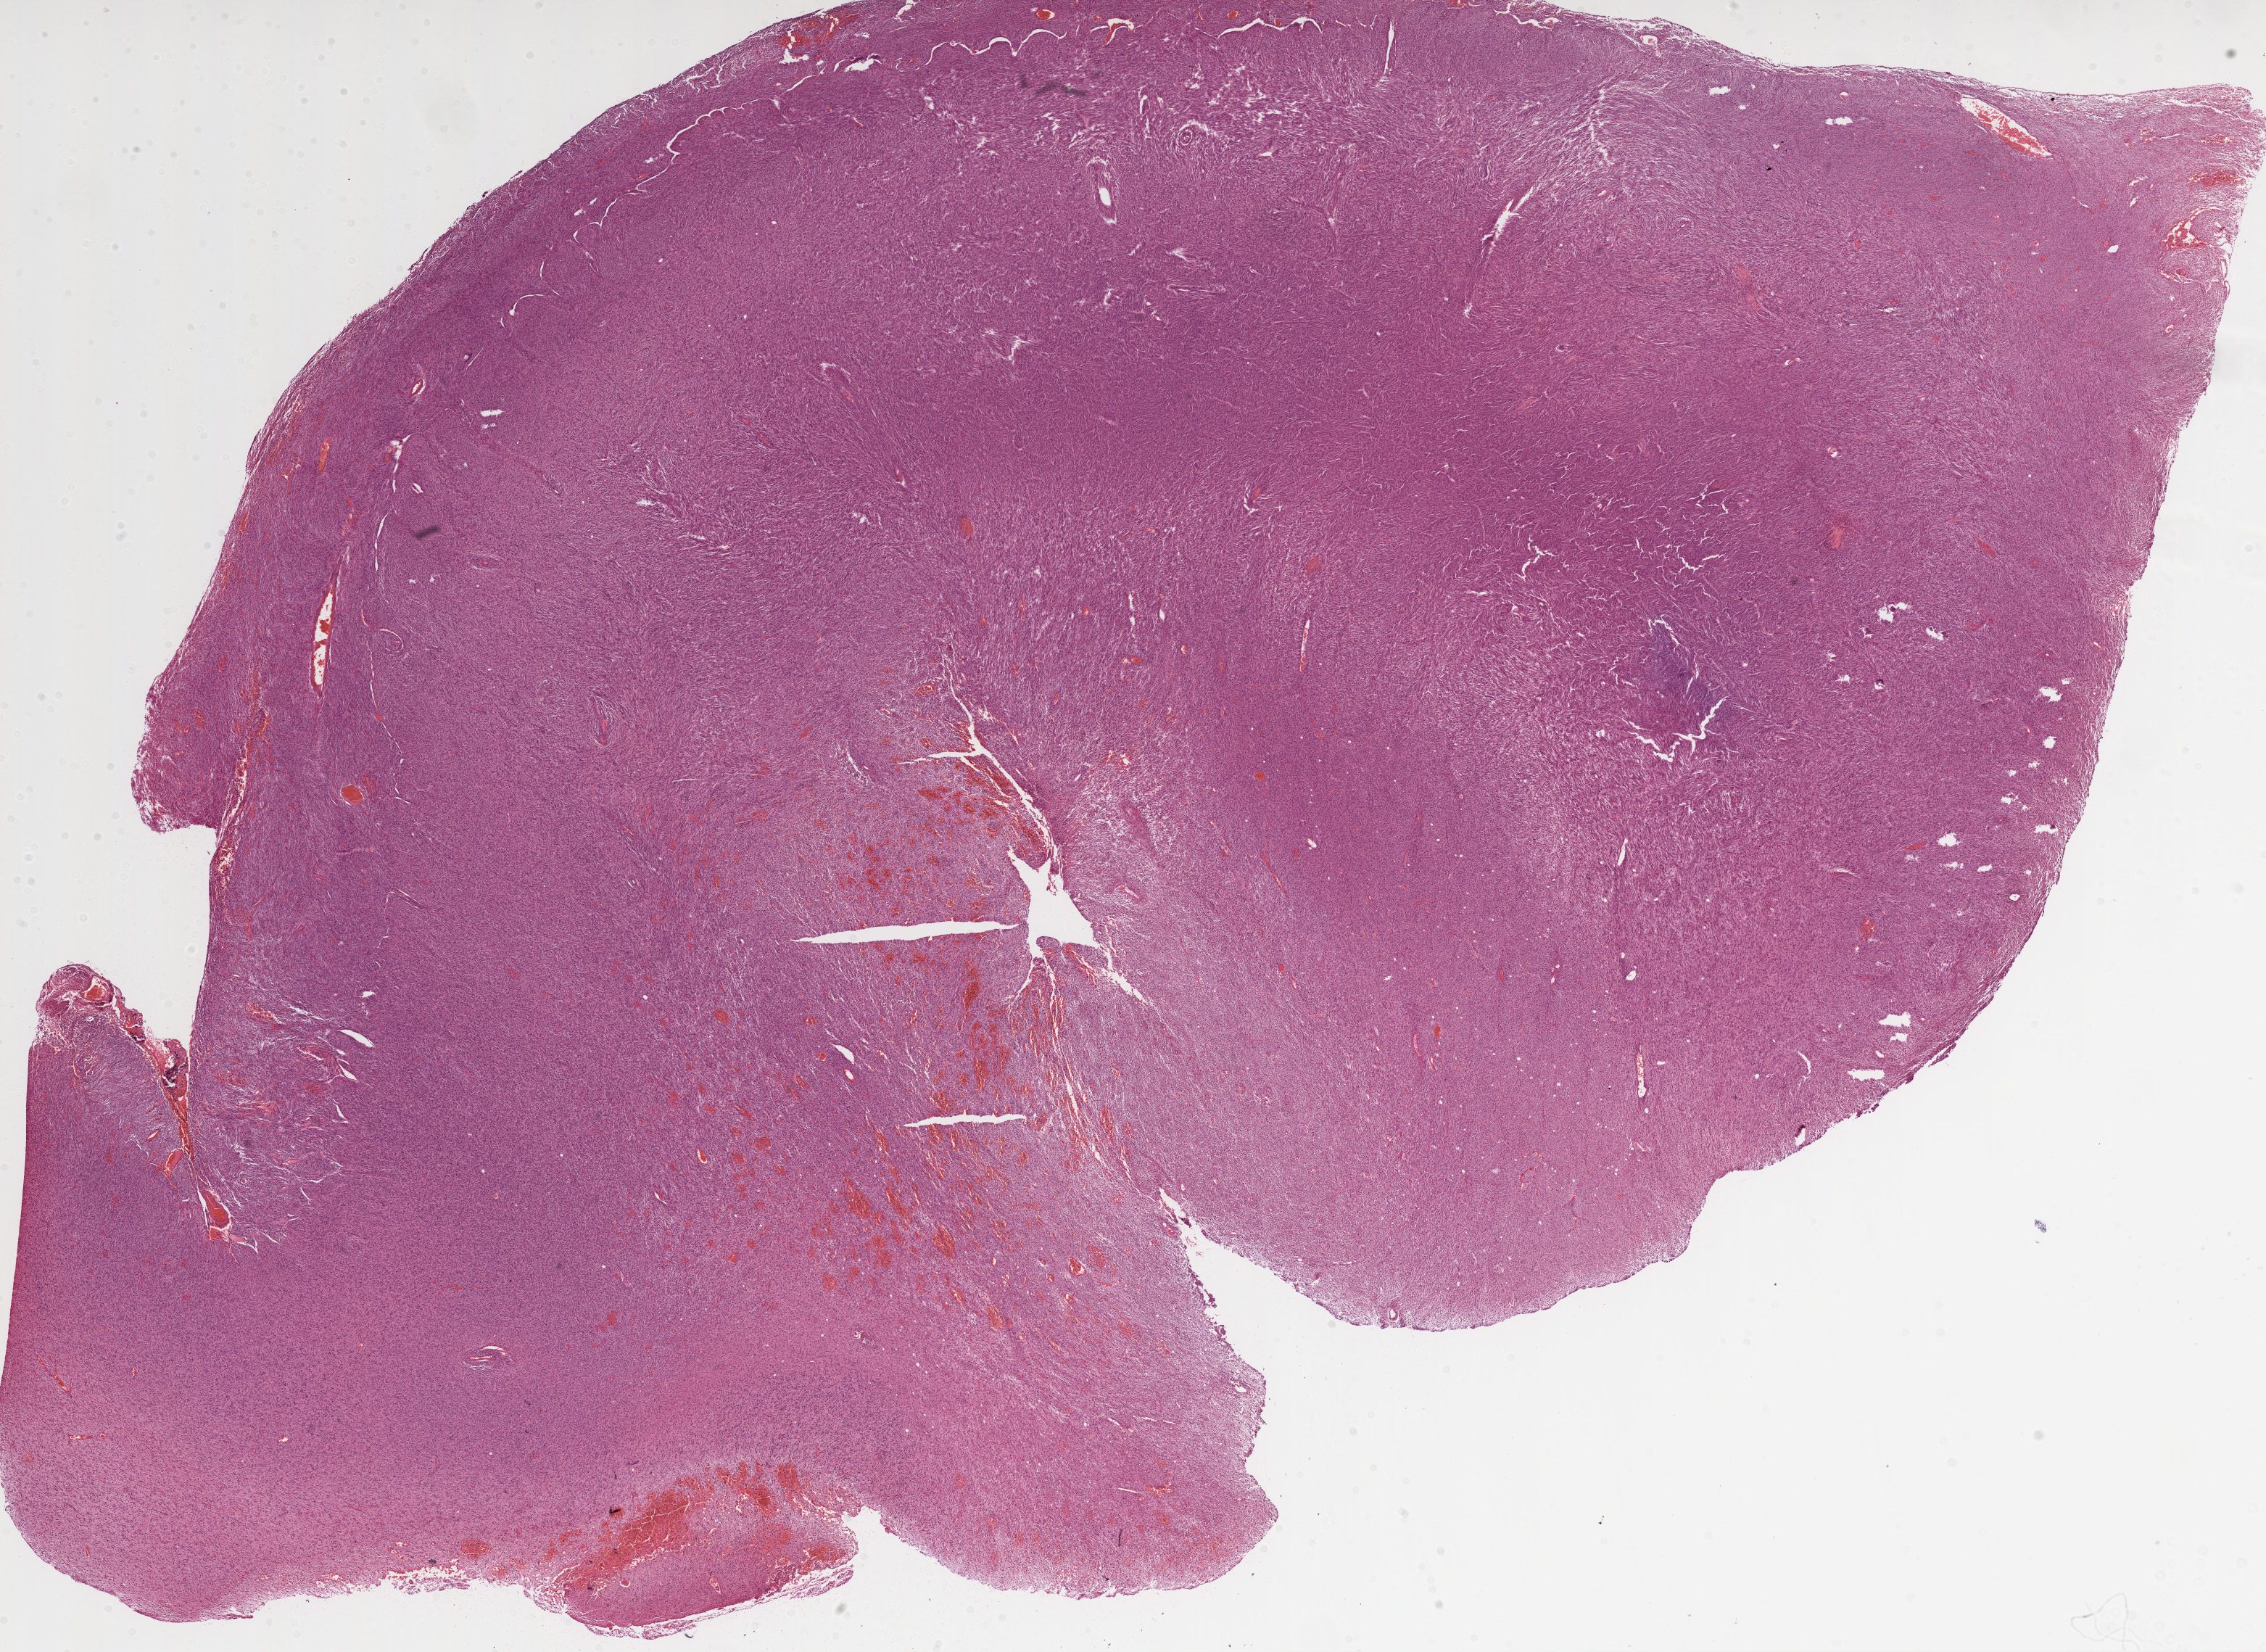
Digitized H&E-stained tissue section (whole slide), whole scanned area (about 25.1 x 18.3 mm, acquisition: 20x scan) shown as a low-resolution overview. Formalin-fixed paraffin-embedded (FFPE) diagnostic section. Primary tumour sample from the brain. Female patient; age at initial diagnosis 62 years.
Pathologic diagnosis: Glioblastoma.